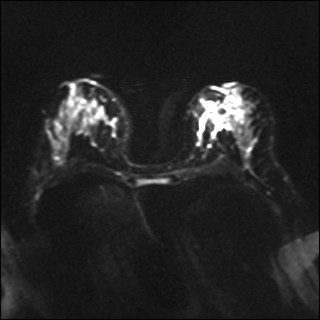
Breast MRI, one axial slice. Slice 16 of 35 in the series (ordered by position). Diffusion-weighted series; image 2 of 4 stored at this slice position (different b-values; order by instance number). 1.5 T. 4 mm slice thickness. 320 × 320 image matrix. Female patient.
Outlined on this slice (expert manual segmentation):
- tumour on diffusion-weighted imaging: bounding box [x1, y1, x2, y2] px = [212, 103, 233, 128]